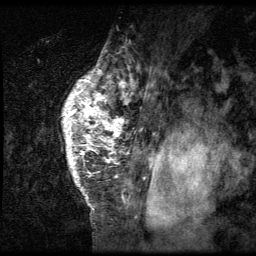
Breast MRI (dynamic contrast-enhanced), one sagittal slice; slice 50 of 64 in the series (ordered by position); 3 images stored at this slice position (order not interpretable as contrast timing); 1.5 T; TE 4.2 ms, TR 9 ms; 2.5 mm slice thickness; 256 × 256 image matrix. Female patient, age 50 years. From the clinical record (not read from this slice): setting: breast cancer imaged before/during neoadjuvant chemotherapy; receptor status: triple-negative.
Annotated regions visible in this slice (semi-automatic segmentation, software-assisted and operator-edited):
- analysis volume of interest (the breast-tissue region the enhancement analysis was run in; not a lesion): bounding box <27,39,138,212> (left, top, right, bottom; pixels)
- tumour enhancement mask (voxels above the 140 % enhancement threshold inside the analysis volume of interest): <63,73,137,207>